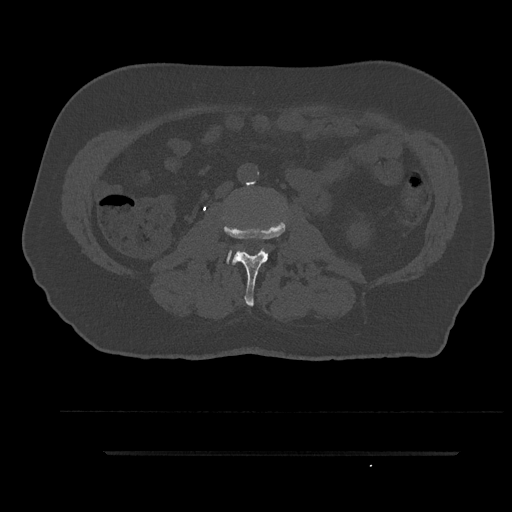
CT including the spine, one axial slice. Slice 86 of 797 in the series (ordered by position). Reconstruction kernel Br40s/3. Bone window (W 1800 / L 400 HU). 0.5 mm slice thickness. 512 × 512 image matrix, field of view 432 × 432 mm. Male patient, age 63 years. From the clinical record (not read from this slice): primary cancer: renal.
Outlined on this slice (semi-automatically segmented with operator editing):
- L2 vertebra: box from (x=224, y=219) to (x=286, y=306) px
- L3 vertebra: (x=226, y=251)–(x=242, y=264)